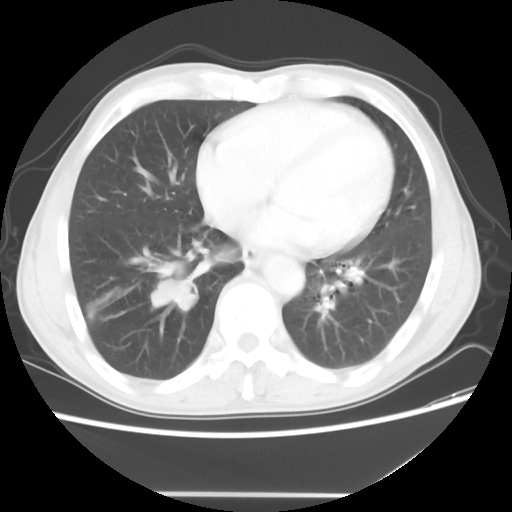
Chest CT, one axial slice; position 20 of 56 along the scan axis; lung window (W 1500 / L -600 HU); 5 mm slice thickness; 512 × 512 image matrix. Male patient, age 65 years. From the clinical record (not read from this slice): clinical TNM (as recorded): T1c N3 M0; histopathological grade: G3.
Structures marked on this image (rectangle marked by the reading radiologist):
- lung tumour (recorded histology: small cell carcinoma): bounding box <145,256,213,311> (left, top, right, bottom; pixels)